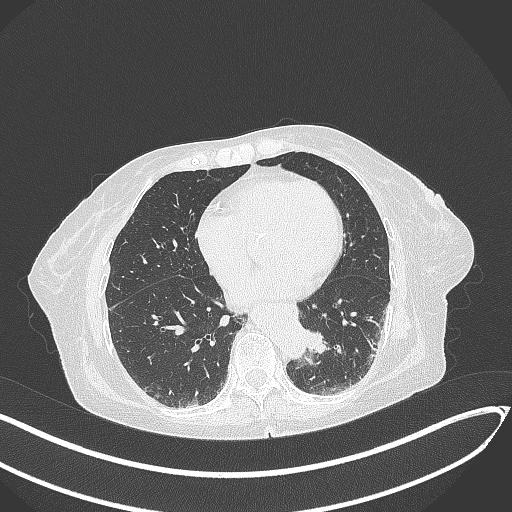
Chest CT, one axial slice; slice 80 of 324 in the series (ordered by position); reconstruction kernel B70f; lung window (W 1500 / L -600 HU); 1 mm slice thickness; 512 × 512 image matrix, field of view 400 × 400 mm. Female patient, age 82 years. Case-level facts recorded for this patient, not image findings: clinical TNM (as recorded): T1b N0 M1.
Outlined on this slice (rectangle marked by the reading radiologist):
- lung tumour (recorded histology: adenocarcinoma): box from (x=301, y=321) to (x=333, y=357) px